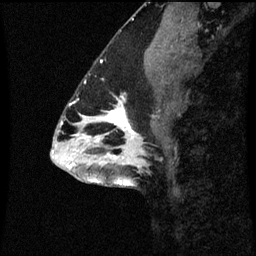
Breast MRI (dynamic contrast-enhanced), one sagittal slice; position 31 of 60 along the scan axis; dynamic contrast-enhanced series, image 2 of 3 at this slice position (ordered by acquisition); 1.5 T; TE 4.2 ms, TR 8.9 ms; 2 mm slice thickness; 256 × 256 image matrix, field of view 200 × 200 mm. Female patient, age 43 years. Case-level facts recorded for this patient, not image findings: setting: breast cancer imaged before/during neoadjuvant chemotherapy; receptor status: HR-positive, HER2-negative.
Outlined on this slice (semi-automatic segmentation, software-assisted and operator-edited):
- analysis volume of interest (the breast-tissue region the enhancement analysis was run in; not a lesion): bounding box <96,96,157,159> (left, top, right, bottom; pixels)
- tumour enhancement mask (voxels above the 70 % enhancement threshold inside the analysis volume of interest): <108,100,137,157>